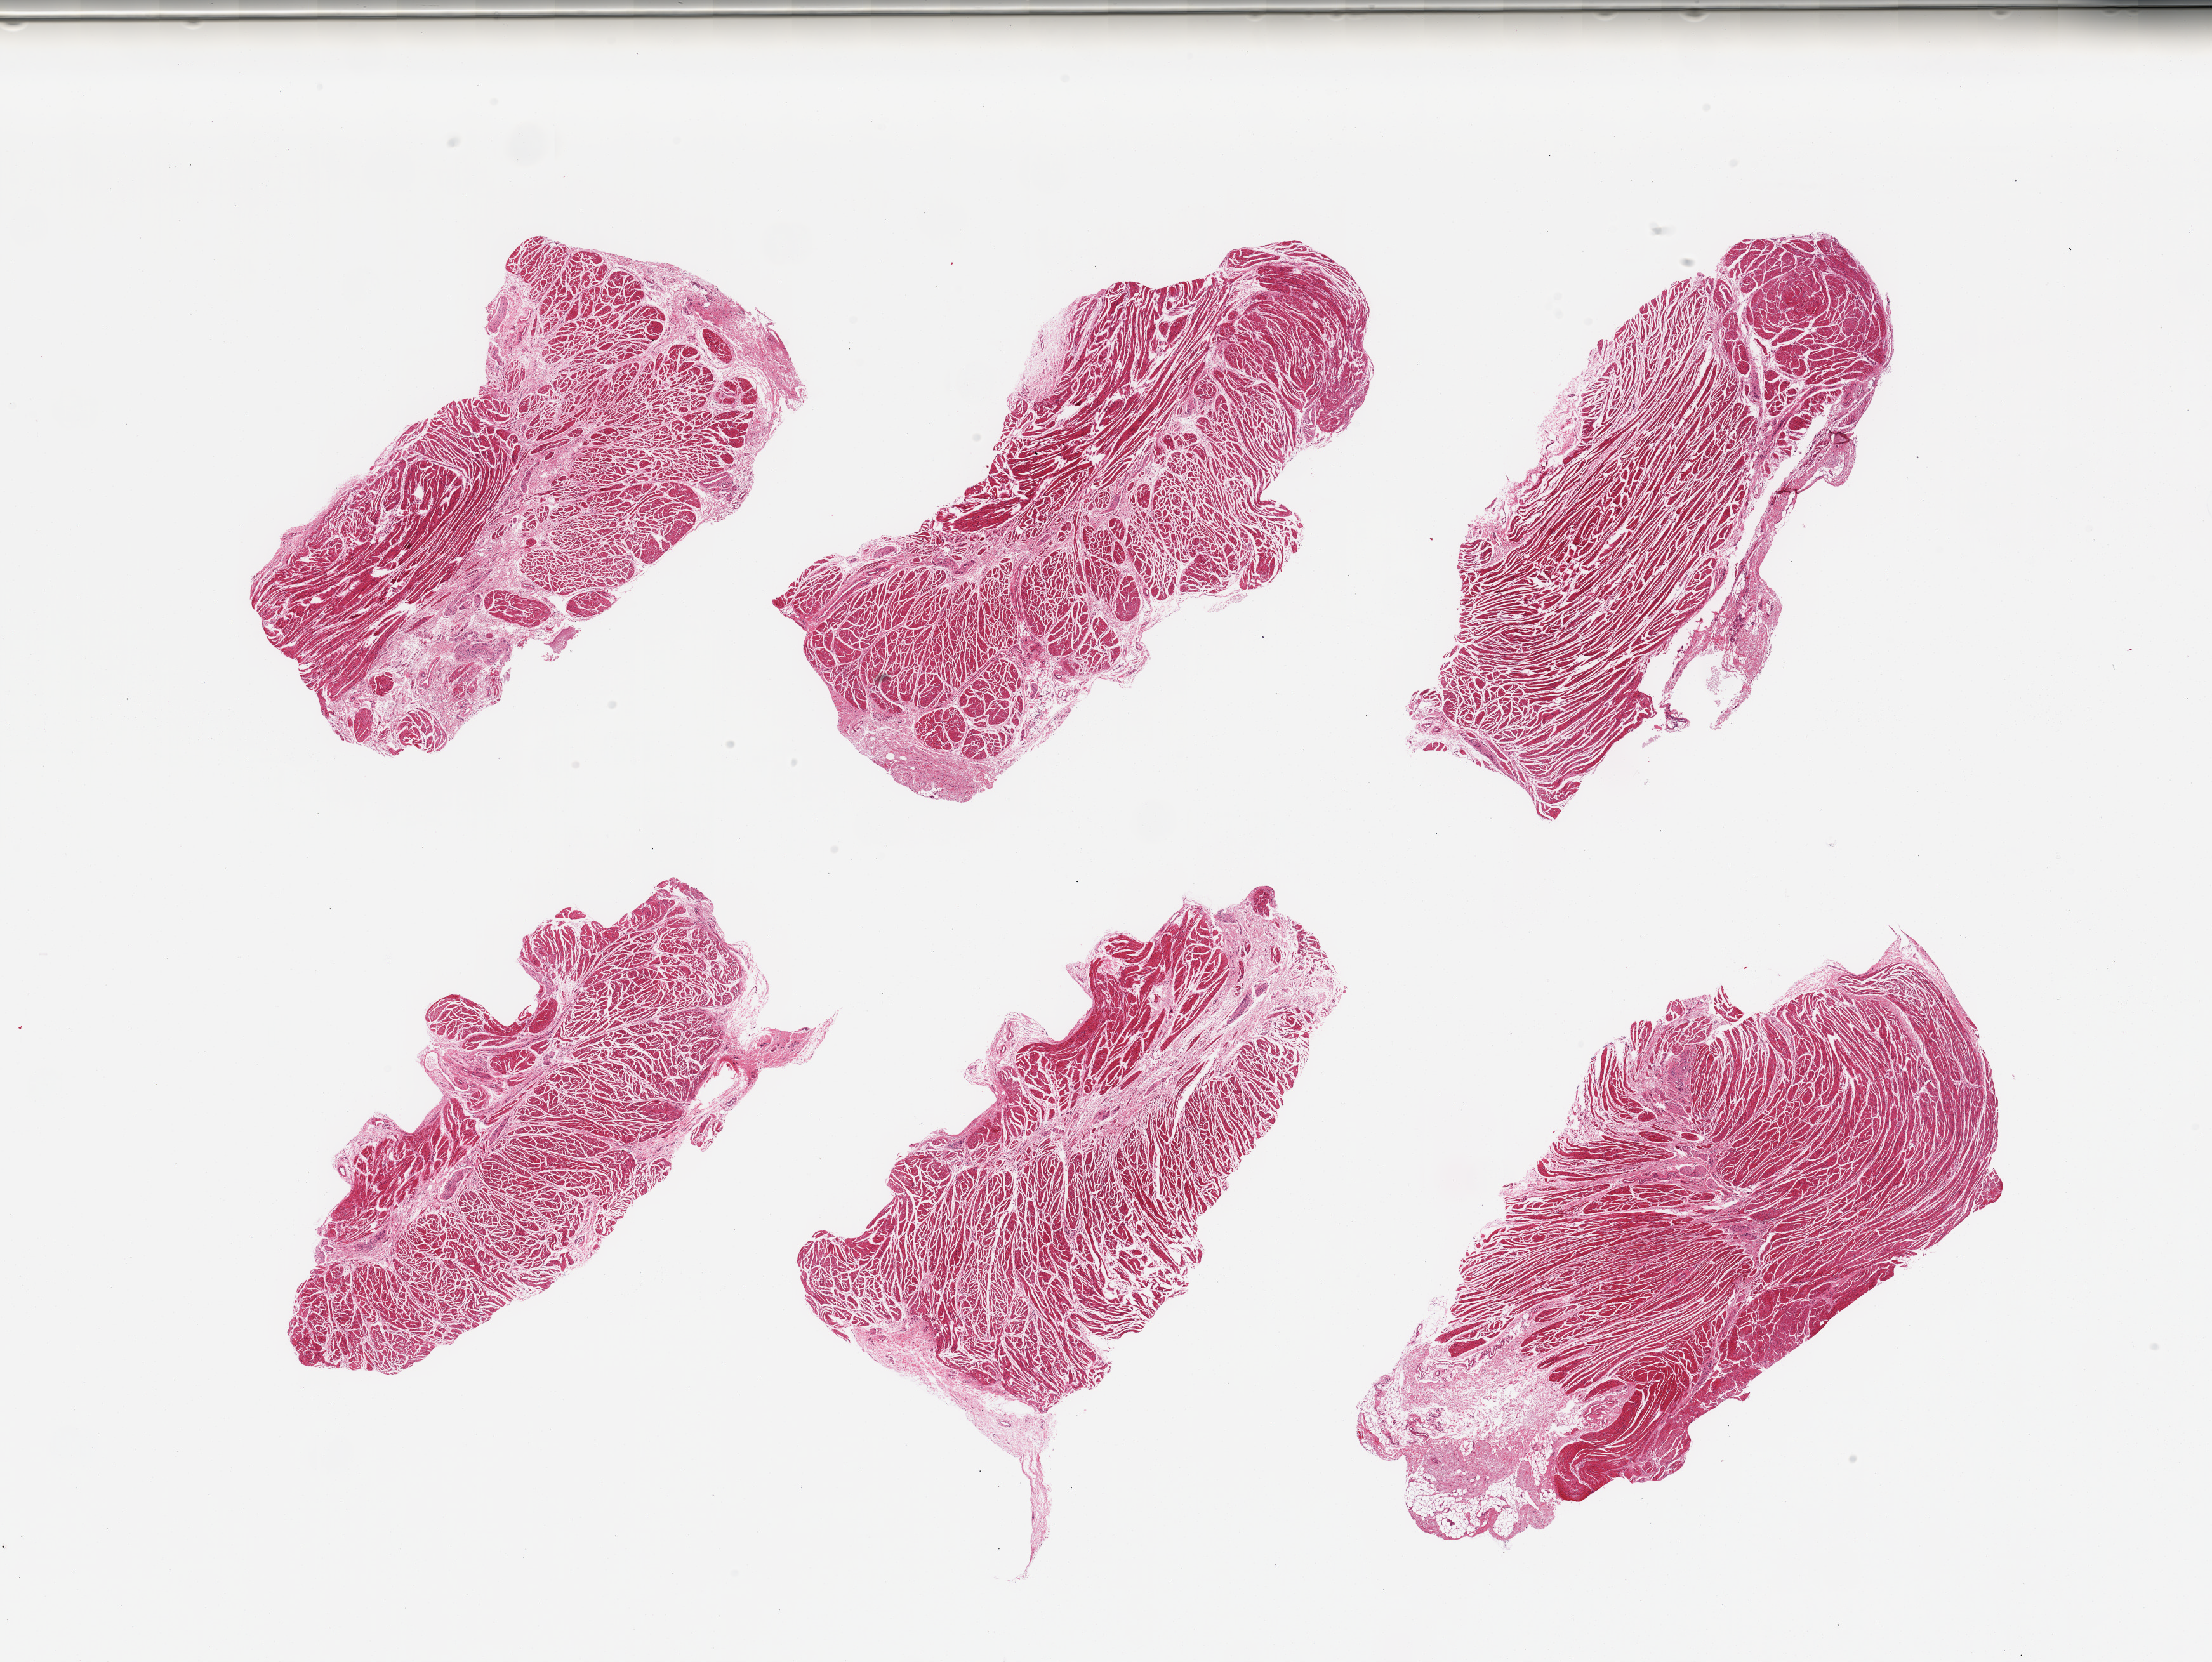
Digitized hematoxylin and eosin (H&E)-stained section — whole scanned area (about 27.6 x 20.7 mm) shown as a low-resolution overview; PAXgene-fixed paraffin-embedded (PFPE) section; target tissue: esophageal muscle; tissue donor sample. Donor: male.
Pathologist's review note for this sample: 6 pieces; target muscularis and serosa.